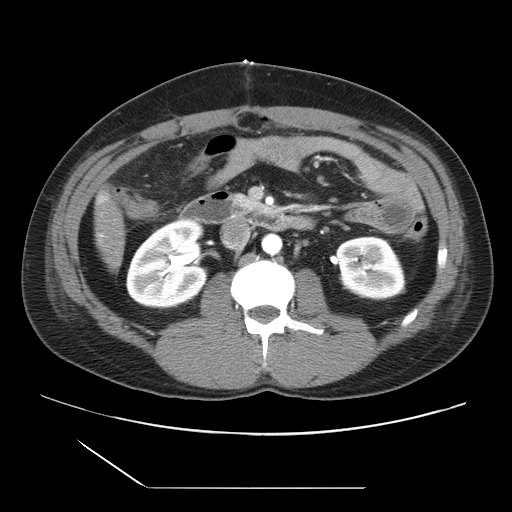
Contrast-enhanced abdominal CT, one axial slice; position 3 of 39 along the scan axis; 120 kVp; intravenous contrast given; soft-tissue window (W 400 / L 40 HU); 5 mm slice thickness; 512 × 512 image matrix, field of view 395 × 395 mm. Male patient, age 39 years. Case-level facts recorded for this patient, not image findings: diagnosis: colorectal cancer liver metastases, imaged before liver resection; multiple liver metastases: yes; largest metastasis: 1.3 cm; disease in both lobes: no.
Annotated regions visible in this slice (manually delineated by an expert):
- liver: bounding box [x1, y1, x2, y2] px = [96, 195, 125, 269]